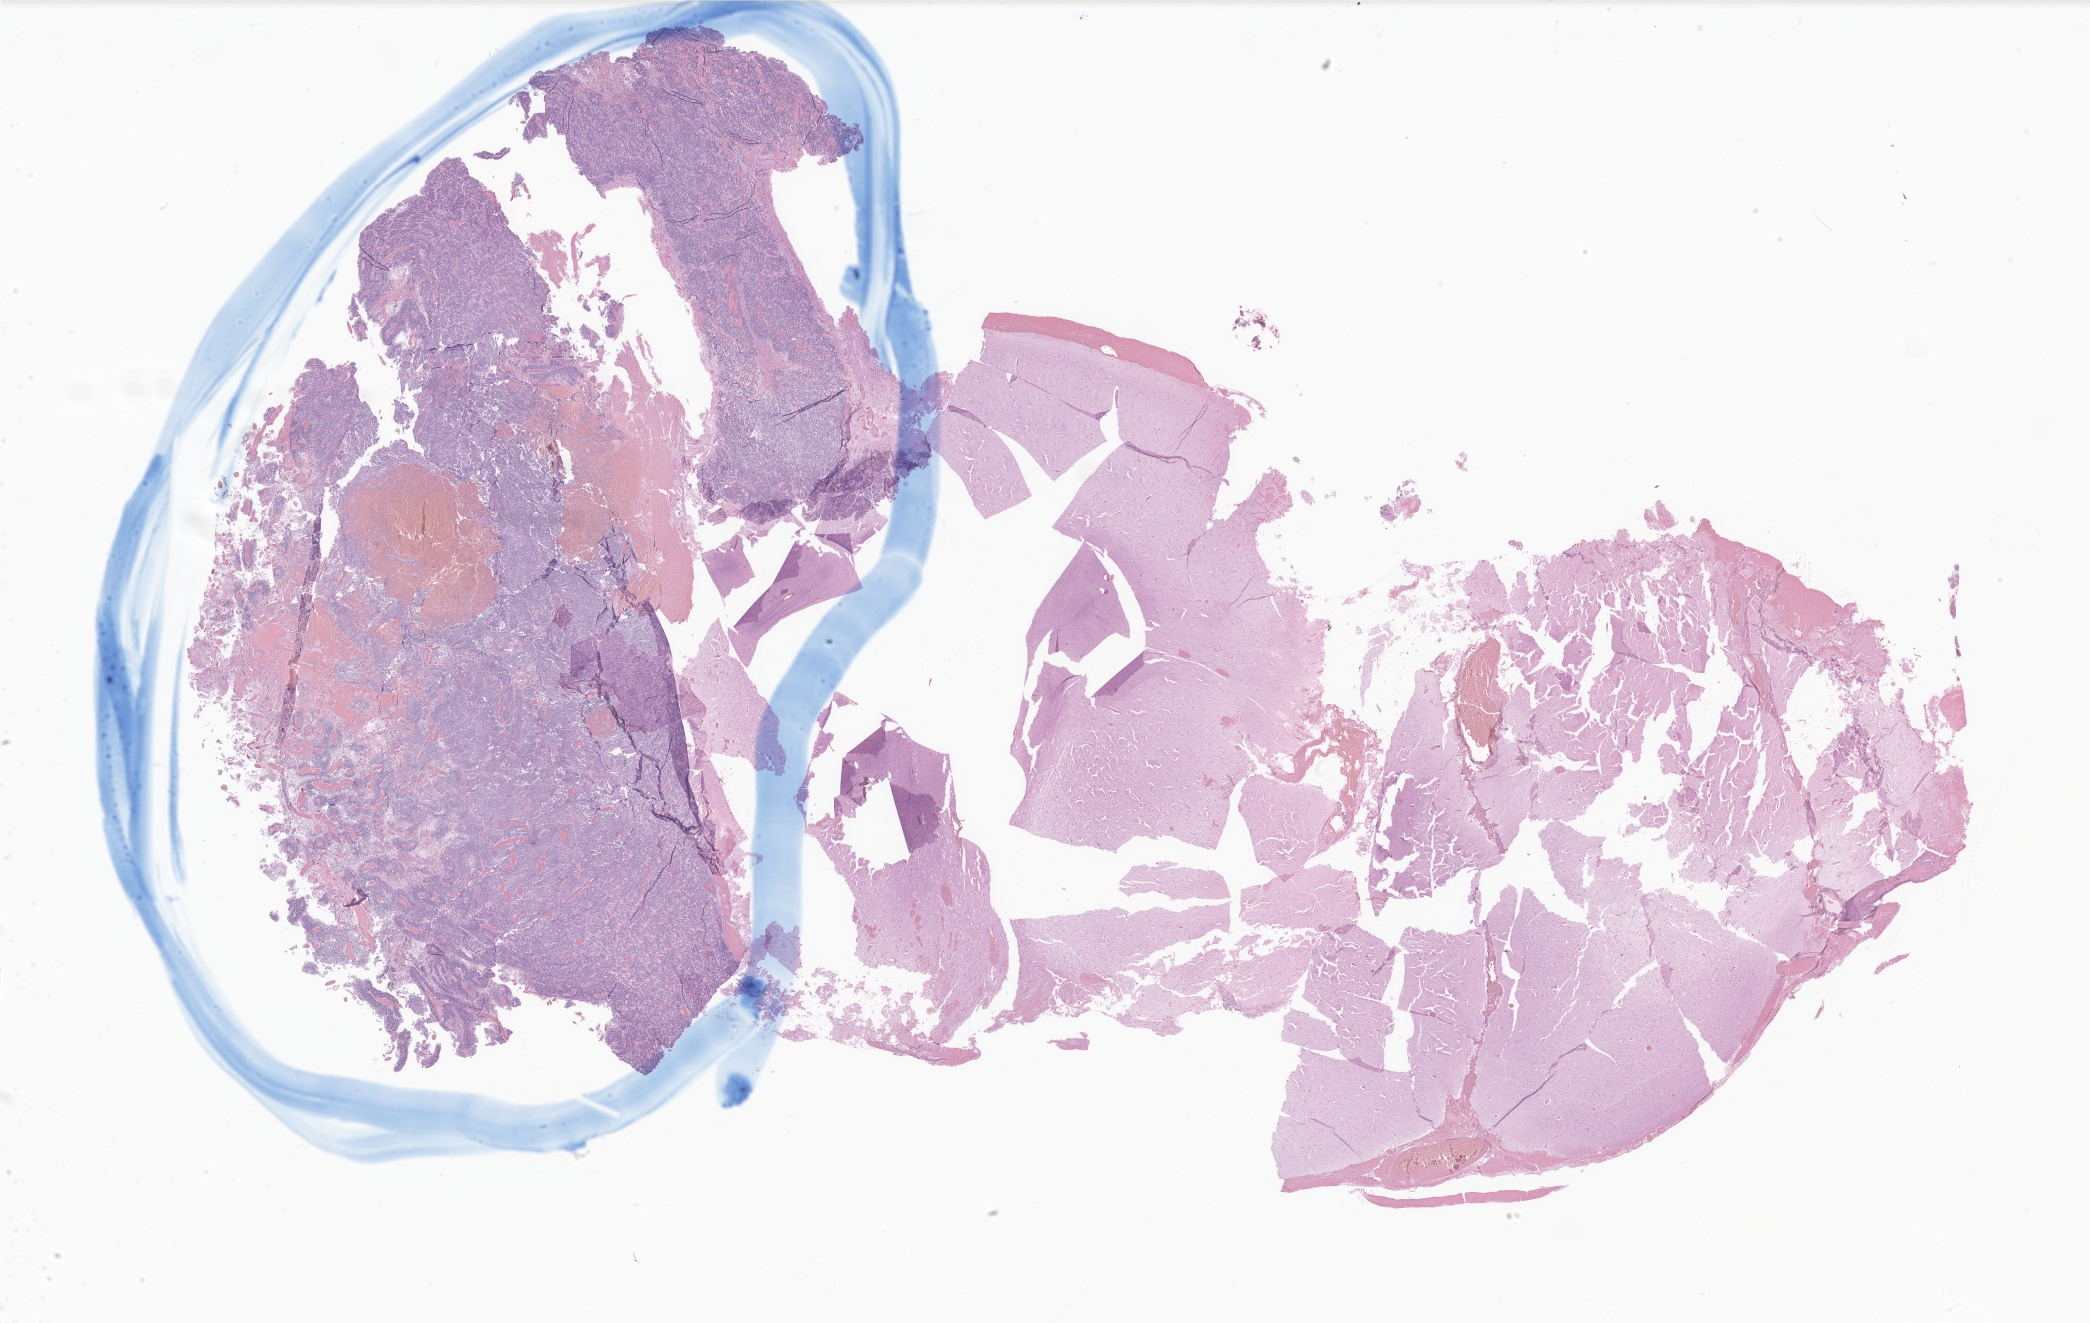
Whole-slide image, hematoxylin and eosin (H&E) stain of tumor tissue from the brain — shown as a low-resolution overview of the whole scanned area (about 35.2 x 22.3 mm), formalin-fixed paraffin-embedded section. Patient male; age 583 days (about 1.6 years).
- diagnosis (ICD-O-3 morphology term): Ependymoma, NOS